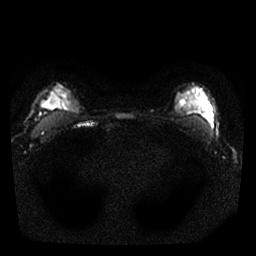
Breast MRI, one axial slice. Slice 21 of 25 in the series (ordered by position). Diffusion-weighted series; image 2 of 4 stored at this slice position (different b-values; order by instance number). 1.5 T. 256 × 256 image matrix. Female patient.
Annotated regions visible in this slice (outlined manually by an expert reader):
- tumour on diffusion-weighted imaging: bounding box <42,90,75,114> (left, top, right, bottom; pixels)